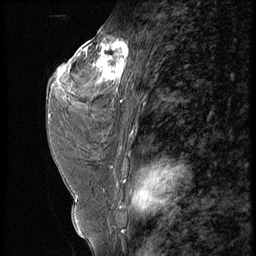
Breast MRI (dynamic contrast-enhanced), one sagittal slice; slice 33 of 56 in the series (ordered by position); 4 images stored at this slice position (order not interpretable as contrast timing); 1.5 T; TE 4.2 ms, TR 9 ms; 2.5 mm slice thickness; 256 × 256 image matrix, field of view 180 × 180 mm. Female patient, age 44 years. From the clinical record (not read from this slice): setting: breast cancer imaged before/during neoadjuvant chemotherapy; receptor status: triple-negative.
Annotated regions visible in this slice (semi-automatically segmented with operator editing):
- analysis volume of interest (the breast-tissue region the enhancement analysis was run in; not a lesion): bounding box (x1, y1, x2, y2) in pixels: (87, 28, 132, 99)
- tumour enhancement mask (voxels above the 140 % enhancement threshold inside the analysis volume of interest): (93, 40, 129, 83)